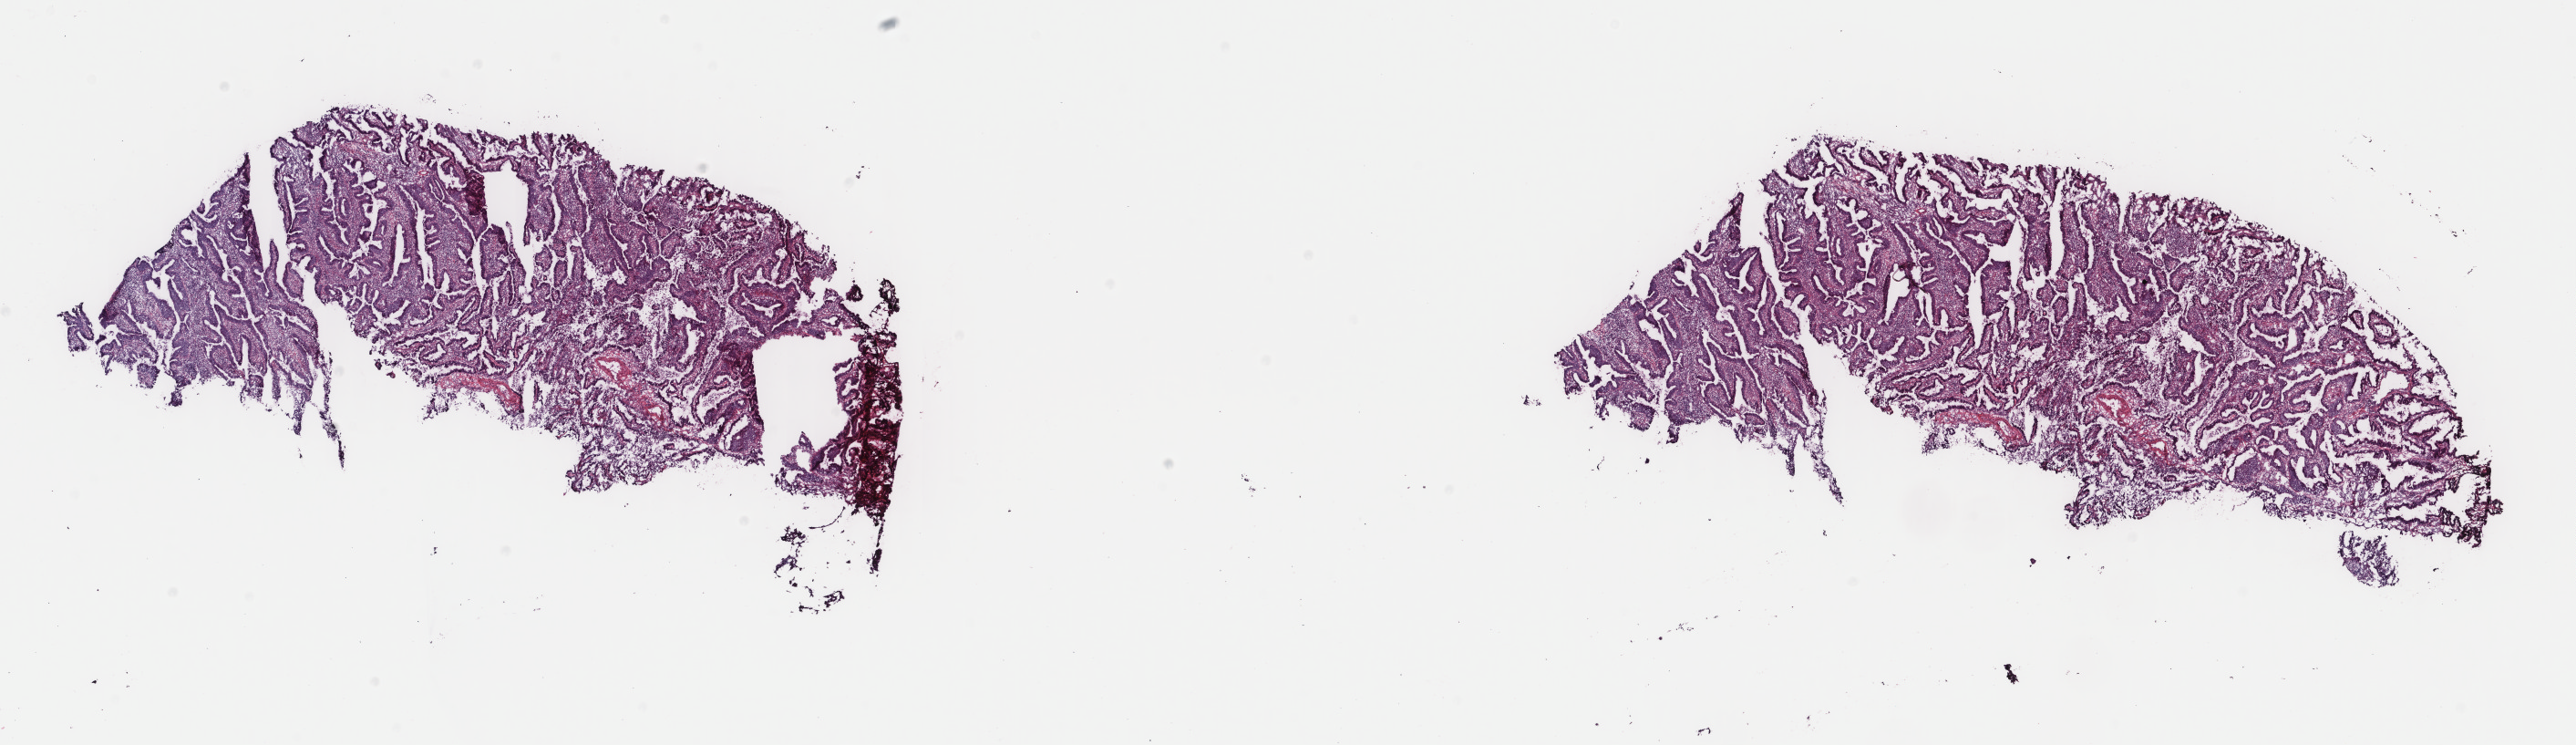
Digitized H&E tissue section (whole slide) — low-resolution overview of the scanned area, about 22.4 x 6.5 mm, frozen section from the top of the tissue portion, primary tumour sample from the cervix. Female, age 37 years at initial diagnosis. Histologic grade: G1 (well differentiated). Slide review estimates, as recorded: tumour cells 100%, tumour nuclei 65%, normal cells 0%, stromal cells 0%, necrosis 0%. Inflammatory infiltration, as recorded: lymphocyte infiltration 0%, monocyte infiltration 0%, neutrophil infiltration 0%.
- FIGO stage: IB2
- histologic diagnosis: Endometrioid adenocarcinoma, NOS (cervix uteri)